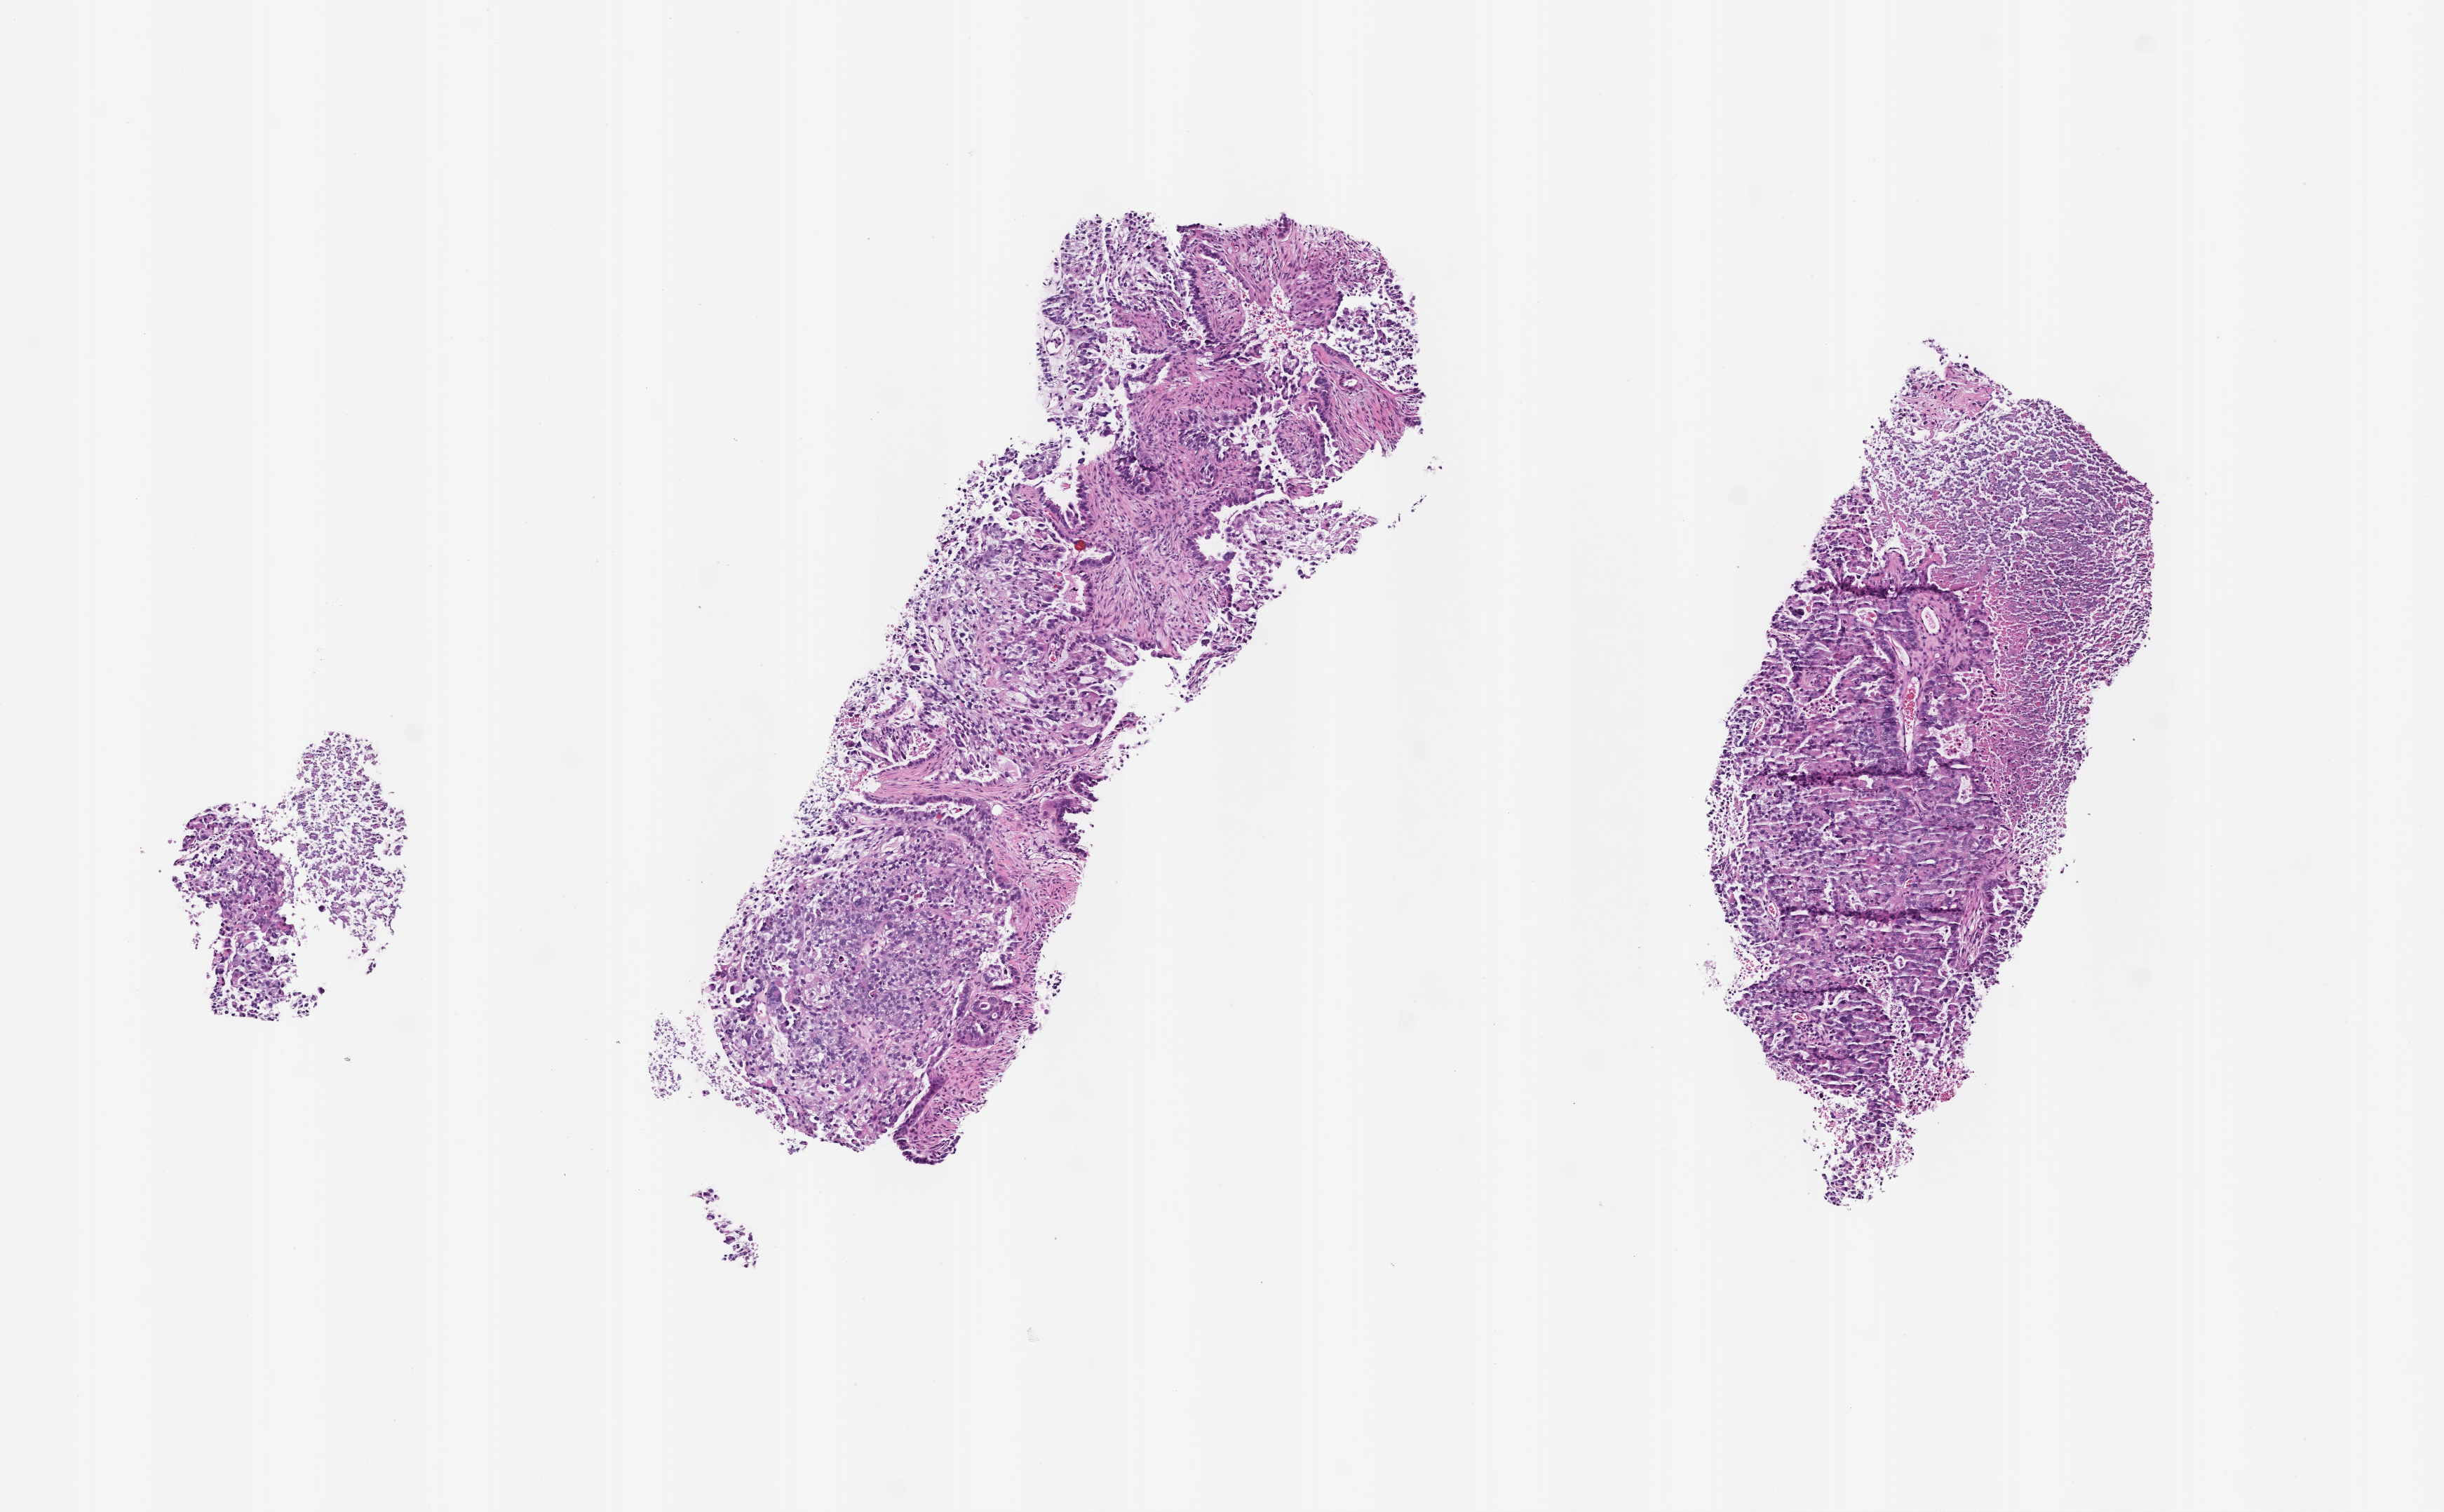
Whole-slide image, haematoxylin and eosin stain, whole scanned area (about 7.0 x 4.4 mm) shown as a low-resolution overview. Formalin-fixed paraffin-embedded section. Tissue site: ovary. Patient: female.
This section: primary tumour tissue. Diagnosis: Ovarian Carcinoma.